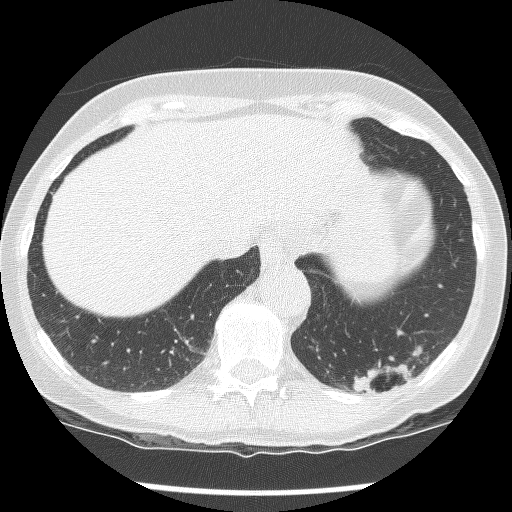
Low-dose screening chest CT, axial slice, second annual screen, lung window (W 1500 / L -600 HU), 512 × 512 image matrix. Female, age 61 years at enrolment. Current smoker at enrolment.
• Lesion marked by an expert reader, box from (x=327, y=310) to (x=440, y=412) px.
• The screening reader recorded 2 non-calcified nodules or masses ≥4 mm on this exam (left lower lobe, left lower lobe); which of them this box marks is not recorded.
• Official screen result: positive, no significant change: stable abnormalities potentially related to lung cancer, unchanged since the prior screening exam.
• Participant outcome: lung cancer diagnosed 585 days after this screen (after the third annual screen) — non-small cell carcinoma, left lower lobe, poorly differentiated (G3), stage IB (AJCC 6th edition), 100 mm at pathology.